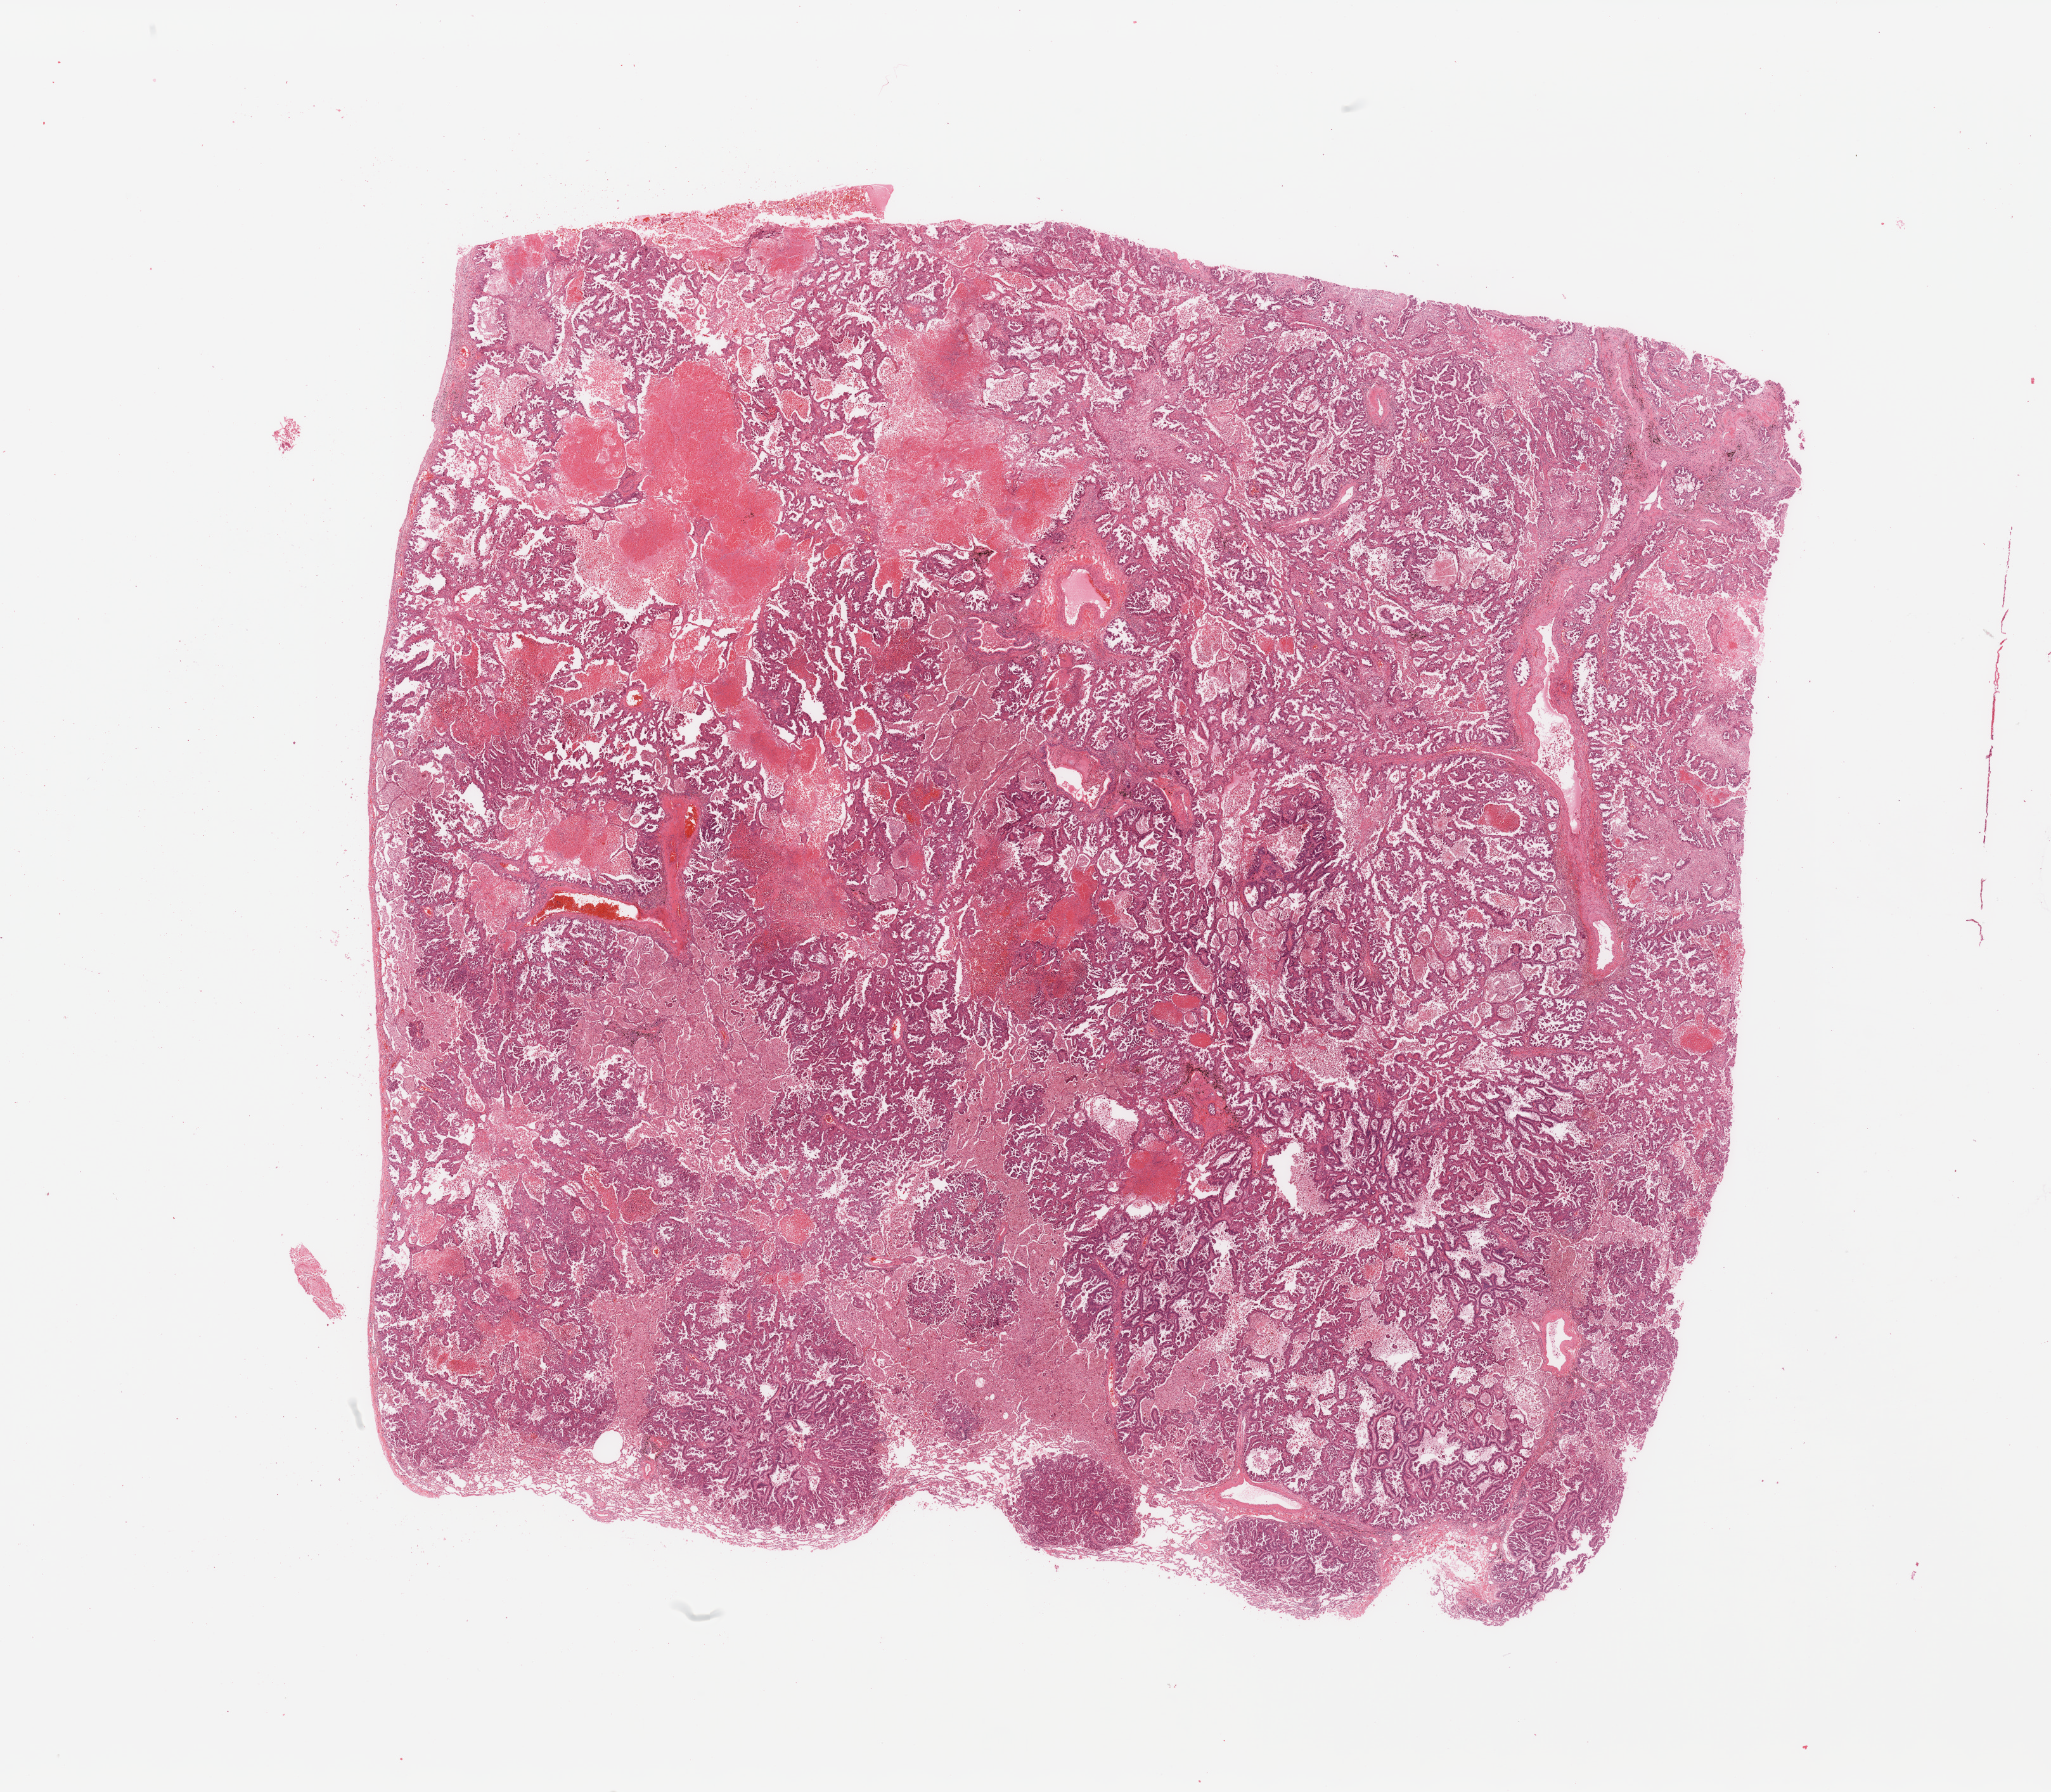
Hematoxylin and eosin (H&E) stained whole-slide image, a low-resolution overview of the entire scanned area, about 25.6 x 22.4 mm. Tumour tissue sample, sampled site: lung. 66-year-old female patient. Histologic grade: G3 (poorly differentiated). Pathologist review of this section (percent, as recorded): tumour nuclei 75%, necrosis 10%.
AJCC pathologic stage: IIB. Histologic diagnosis: Adenocarcinoma, NOS.